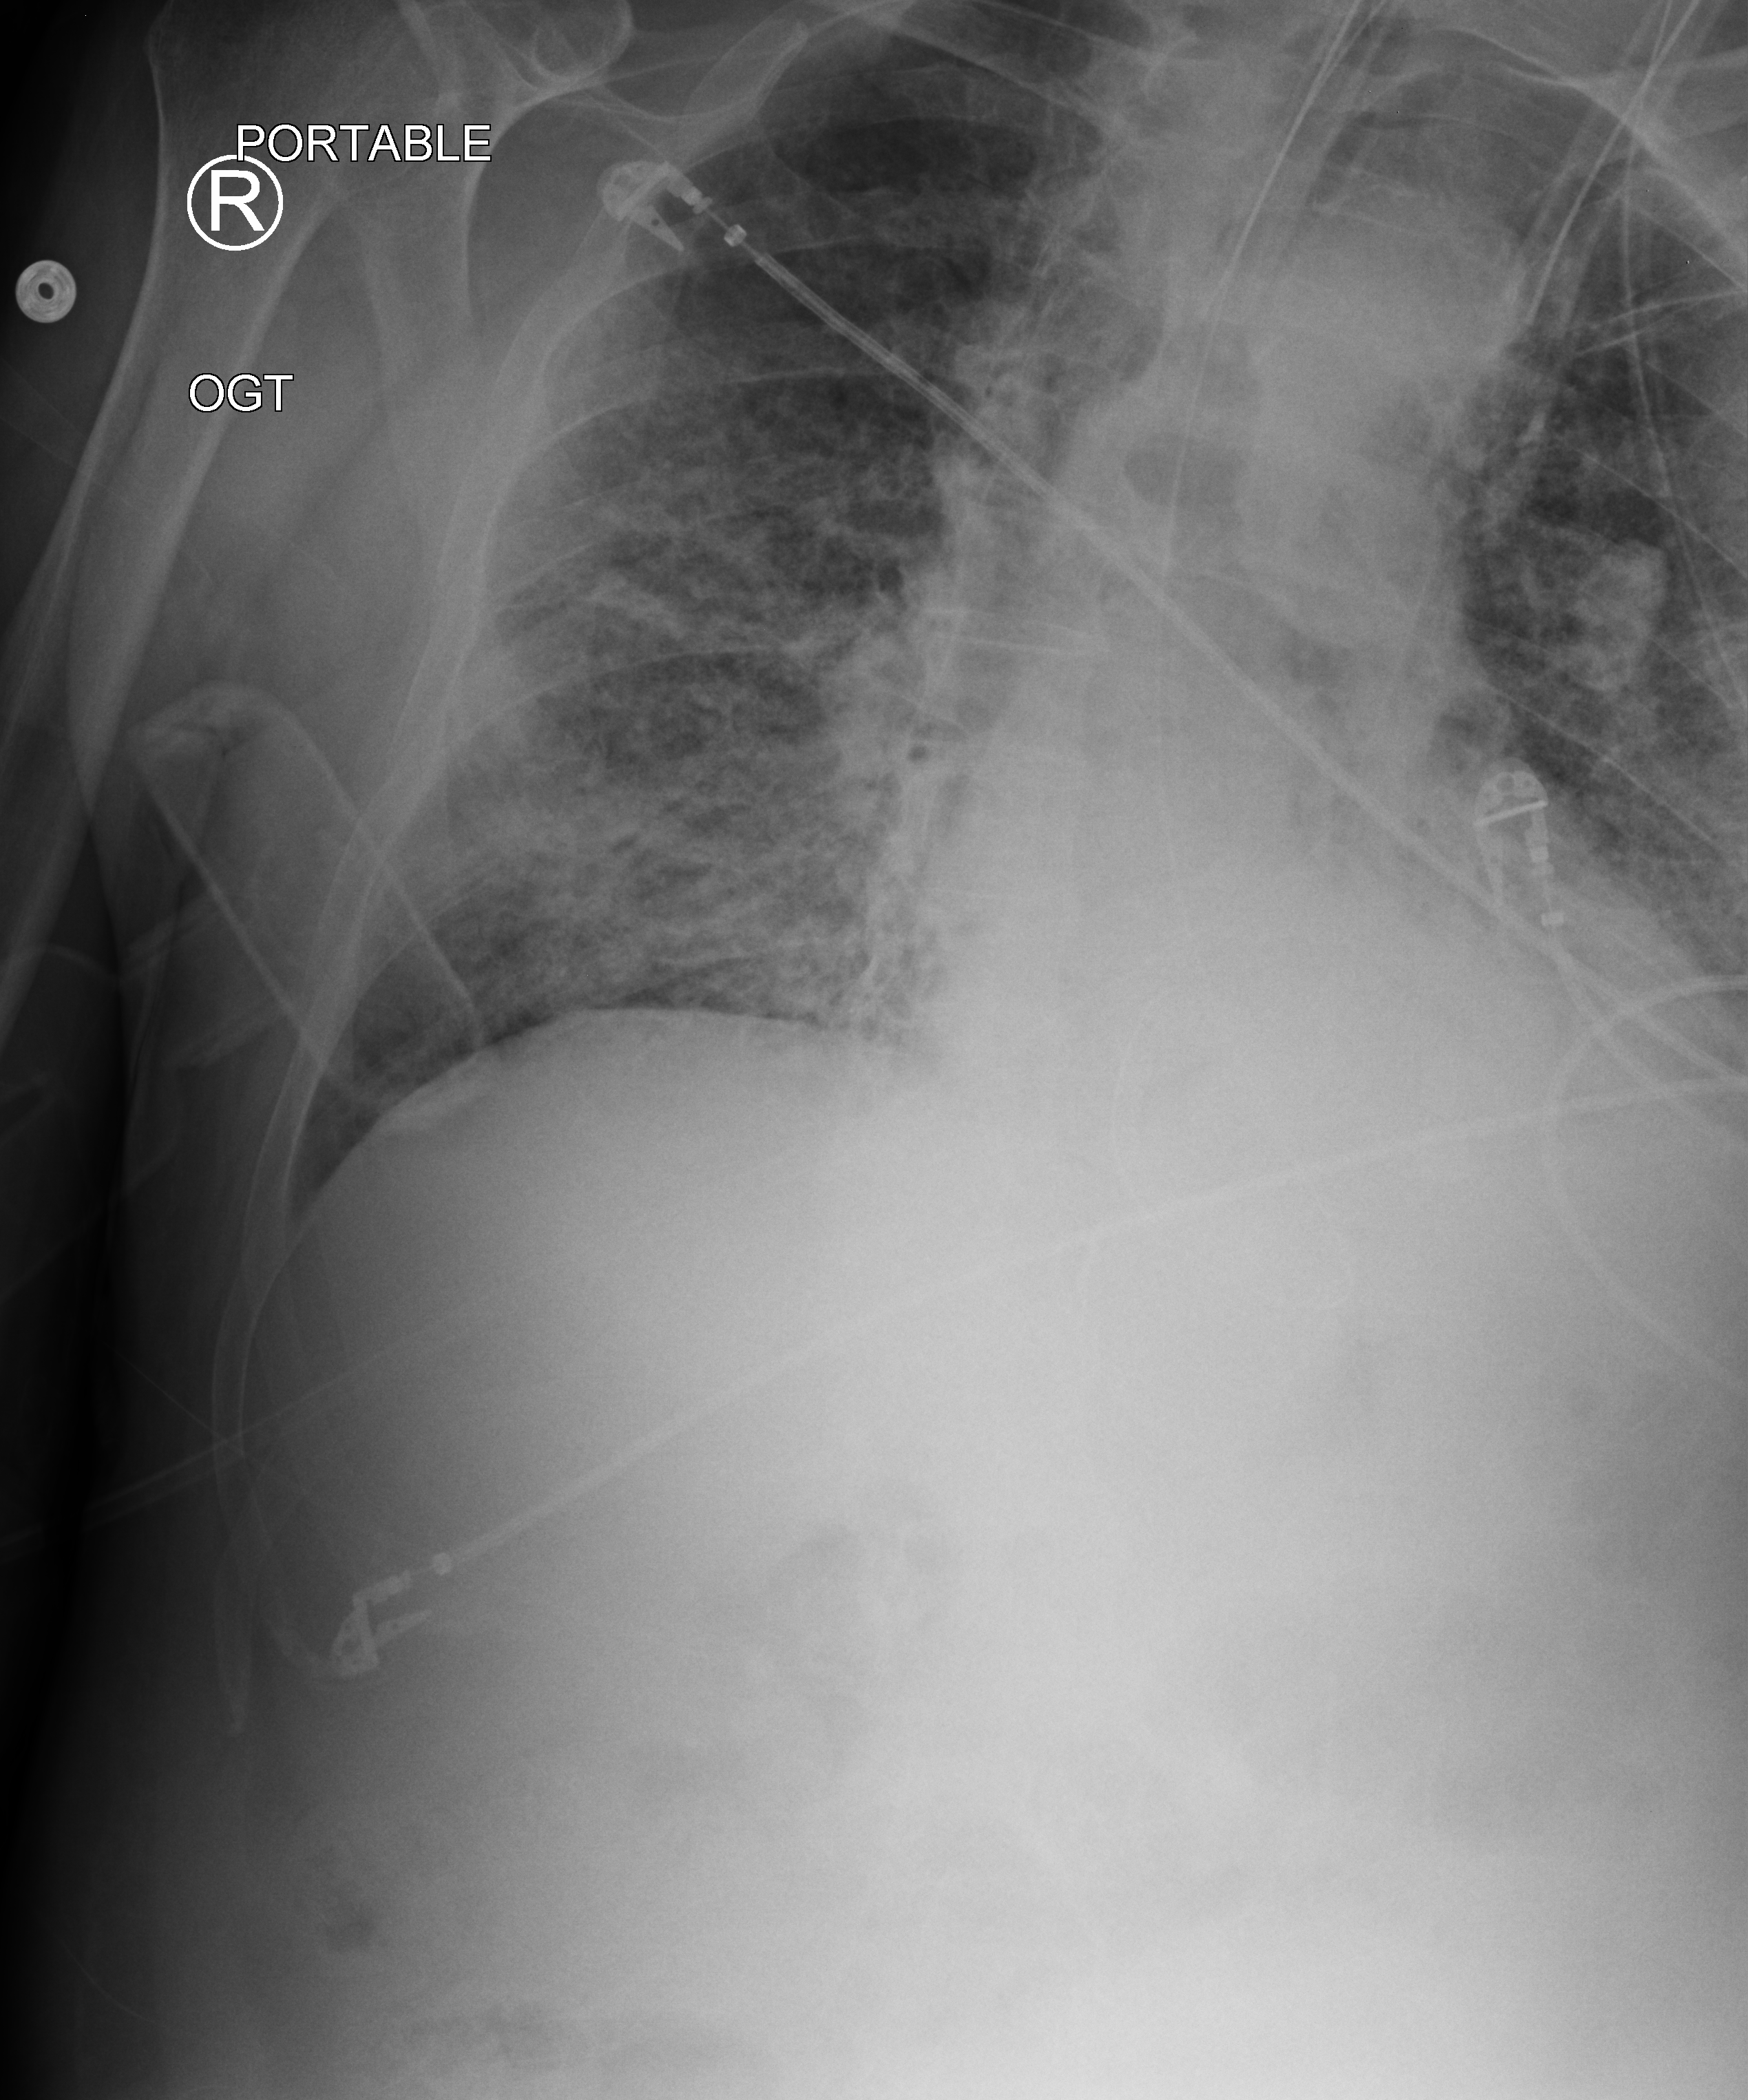
Portable chest radiograph; anteroposterior (AP) projection. Patient hospitalised with COVID-19; male, aged 75–90 years.
From the hospital-stay record, not from the radiograph (when in the stay this image was taken is not recorded):
- hypertension (admission record): no
- mechanically ventilated during this hospital stay: yes